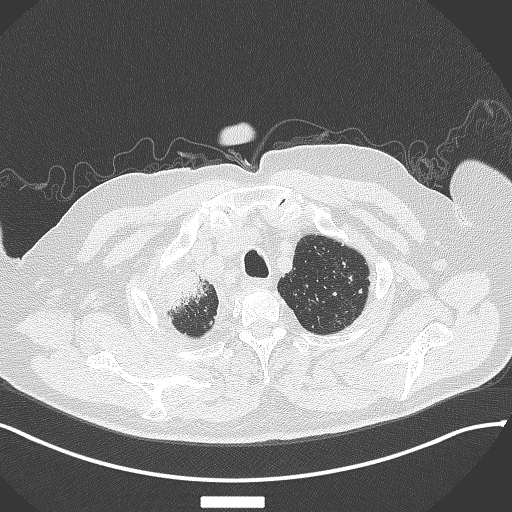
Chest CT, one axial slice. Slice 328 of 384 in the series (ordered by position). Reconstruction kernel B70f. Lung window (W 1500 / L -600 HU). 512 × 512 image matrix, field of view 400 × 400 mm. Patient: male, 69 years. Case-level facts recorded for this patient, not image findings: clinical TNM (as recorded): T4 N3 M1.
Outlined on this slice (rectangle marked by the reading radiologist):
- lung tumour (recorded histology: adenocarcinoma): box from (x=153, y=264) to (x=212, y=315) px